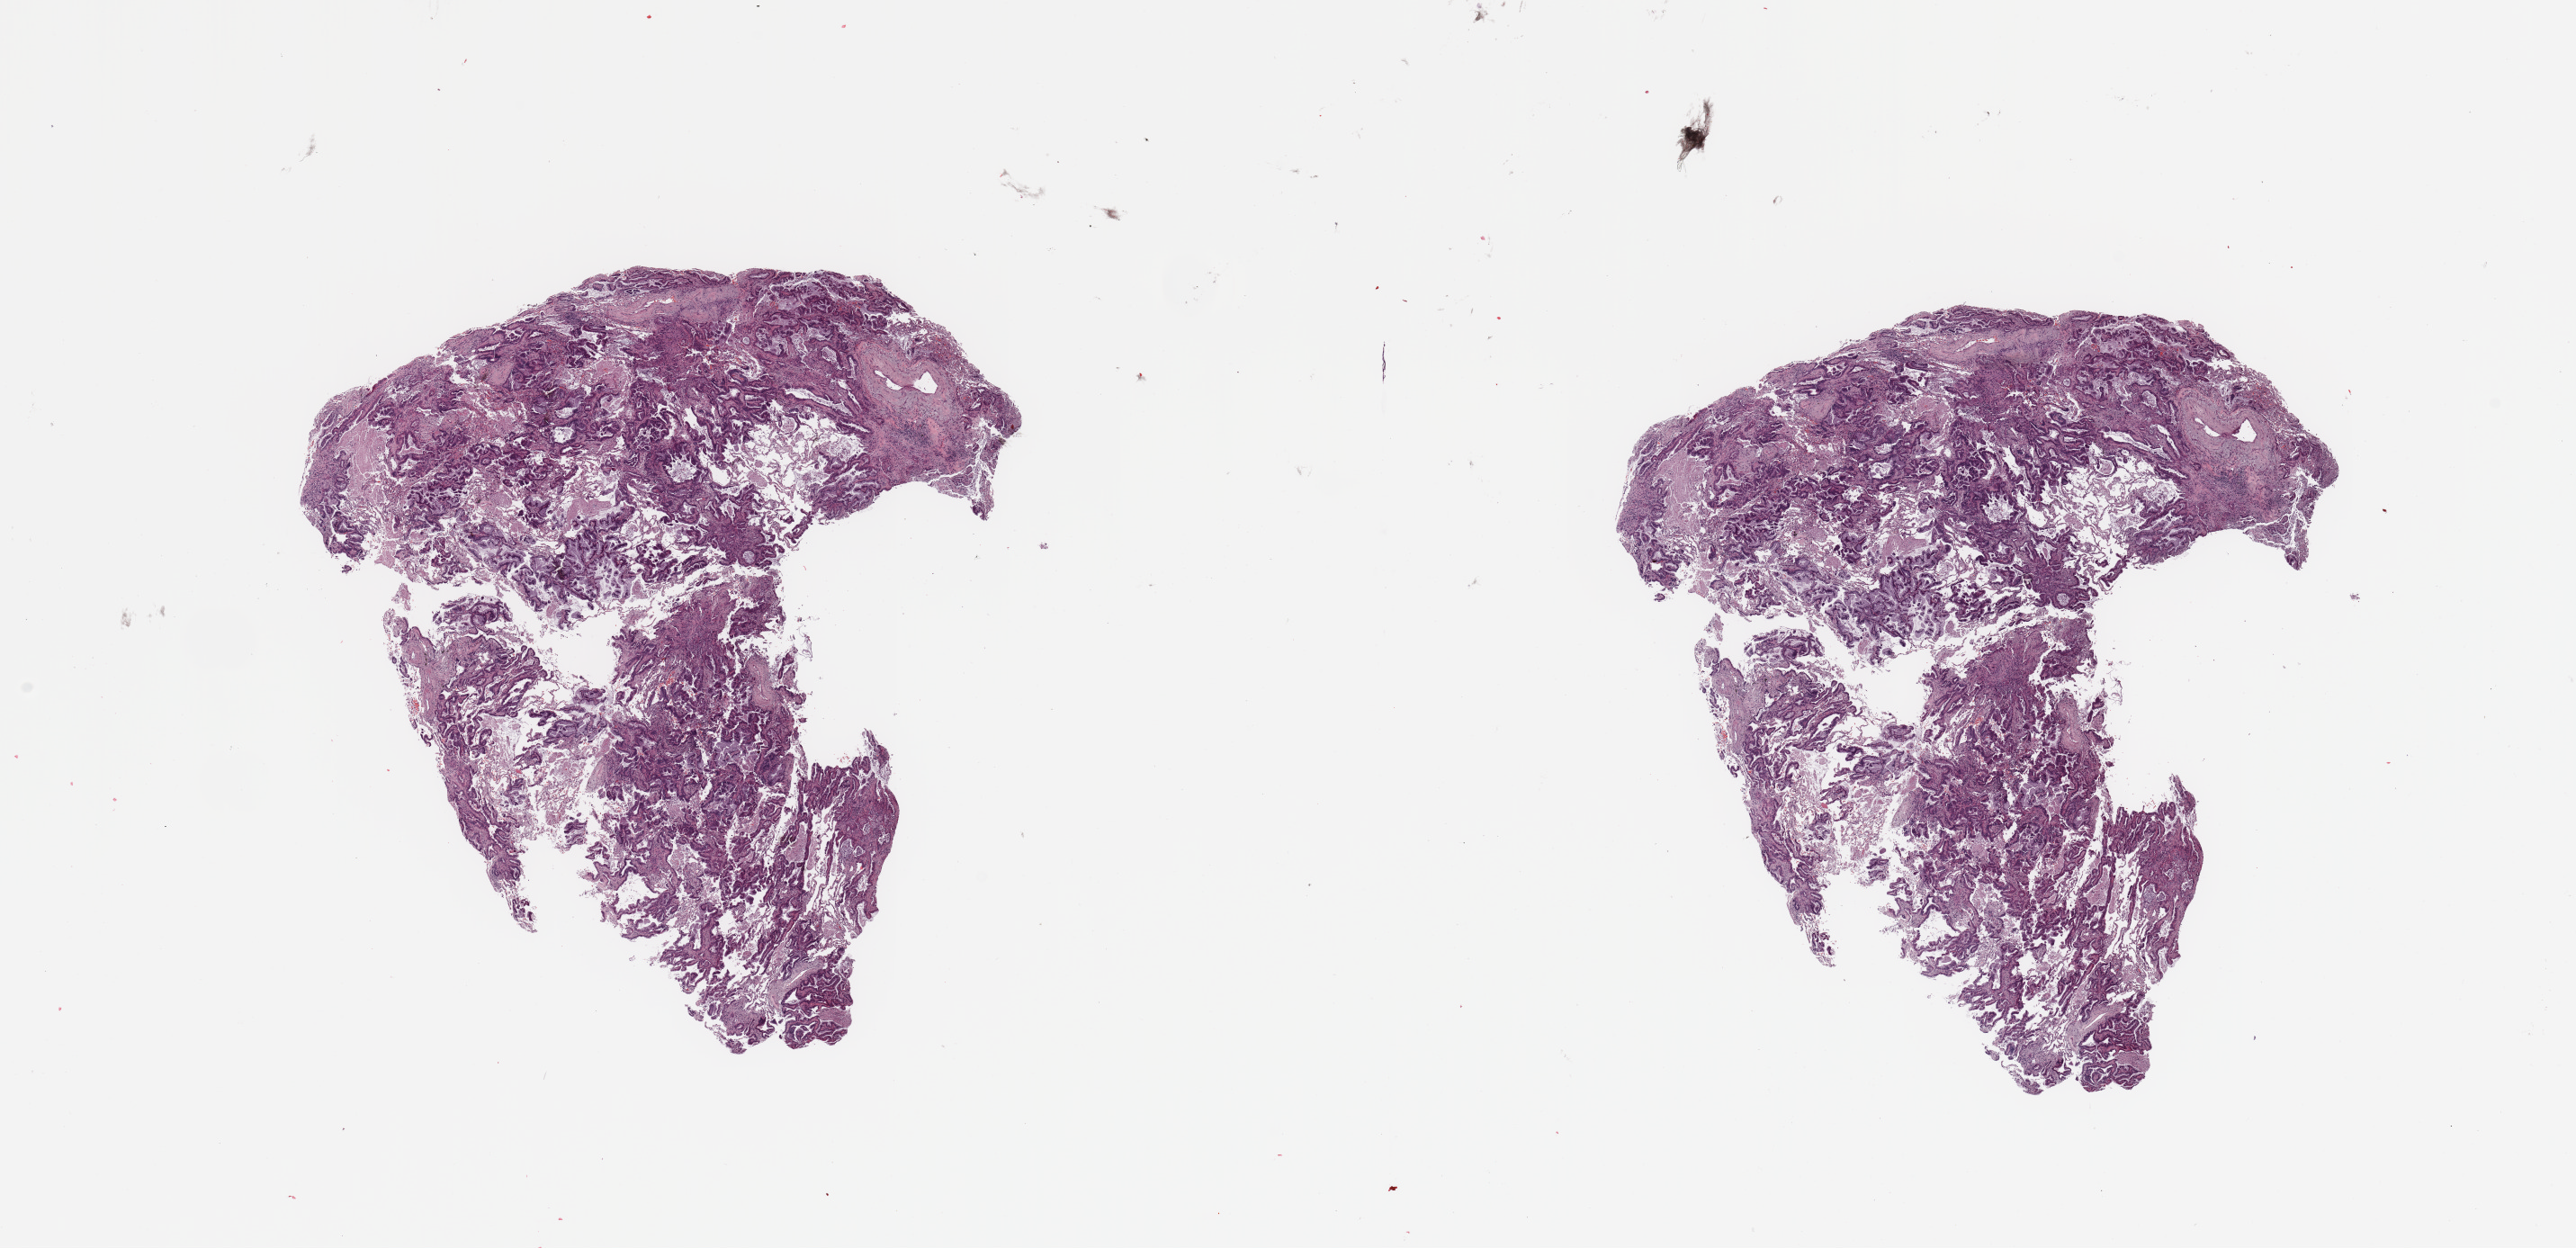
Whole-slide histology image, Hematoxylin and eosin (H&E) stained — shown as a low-resolution overview of the whole scanned area (about 22.6 x 11.0 mm); tumour tissue sample, lung. 79-year-old female patient. Histologic grade: G1 (well differentiated).
Histologic diagnosis: Adenocarcinoma, NOS. AJCC pathologic stage: IIB.